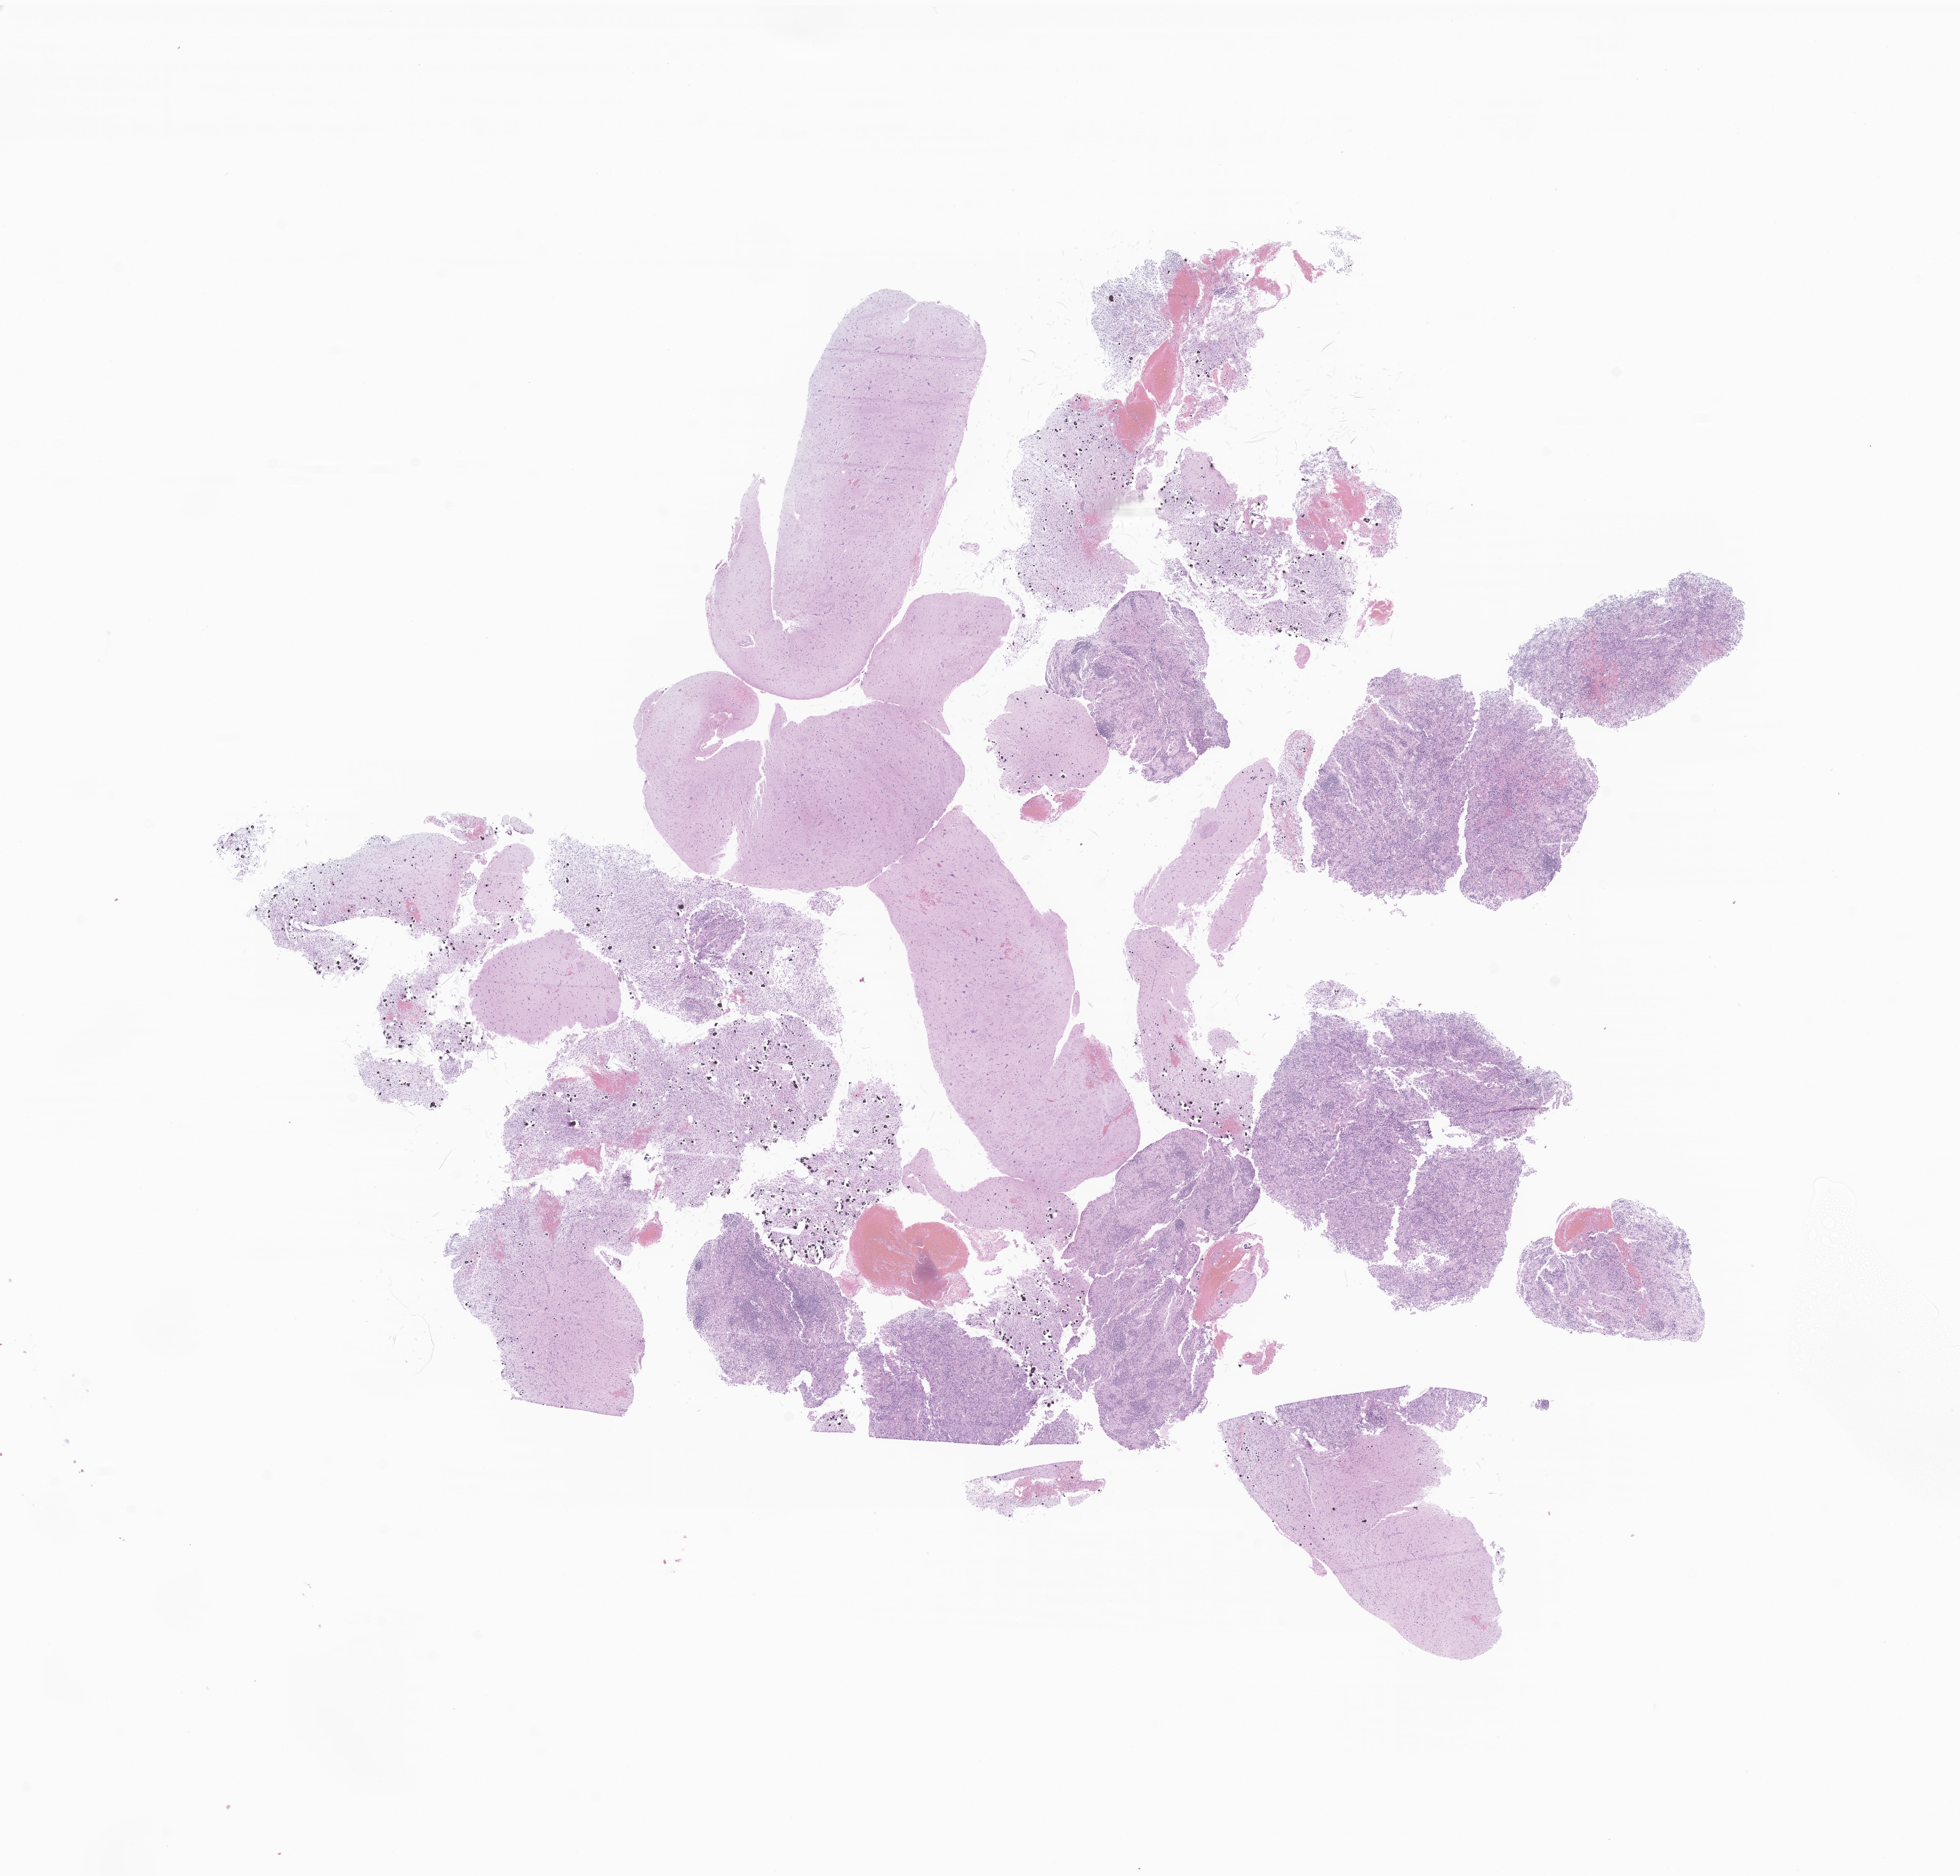
H&E whole-slide image of tumor tissue from the central nervous system — low-resolution overview of the scanned area, about 16.8 x 16.1 mm; formalin-fixed, paraffin-embedded (FFPE) tissue. Female patient, age 96 months (8 years).
Diagnosis (ICD-O-3 morphology term): Ganglioglioma, NOS.